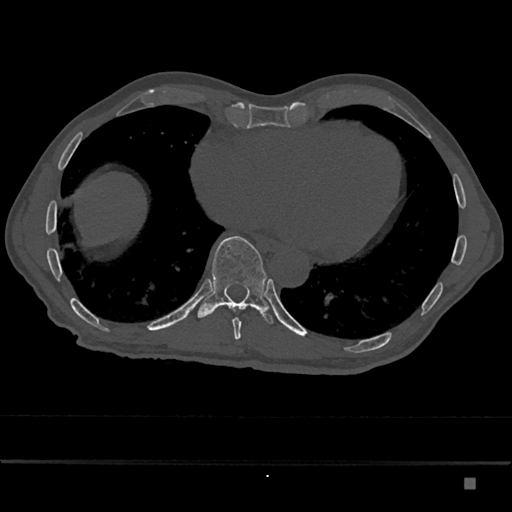
CT including the spine, one axial slice. Slice 762 of 797 in the series (ordered by position). Reconstruction kernel Br40s/3. 120 kVp. Bone window (W 1800 / L 400 HU). 512 × 512 image matrix. Patient: male, 72 years. Case-level facts recorded for this patient, not image findings: primary cancer: prostate.
Outlined on this slice (semi-automatic segmentation, software-assisted and operator-edited):
- T10 vertebra: bounding box [x1, y1, x2, y2] px = [197, 236, 274, 324]
- T9 vertebra: [232, 309, 244, 340]